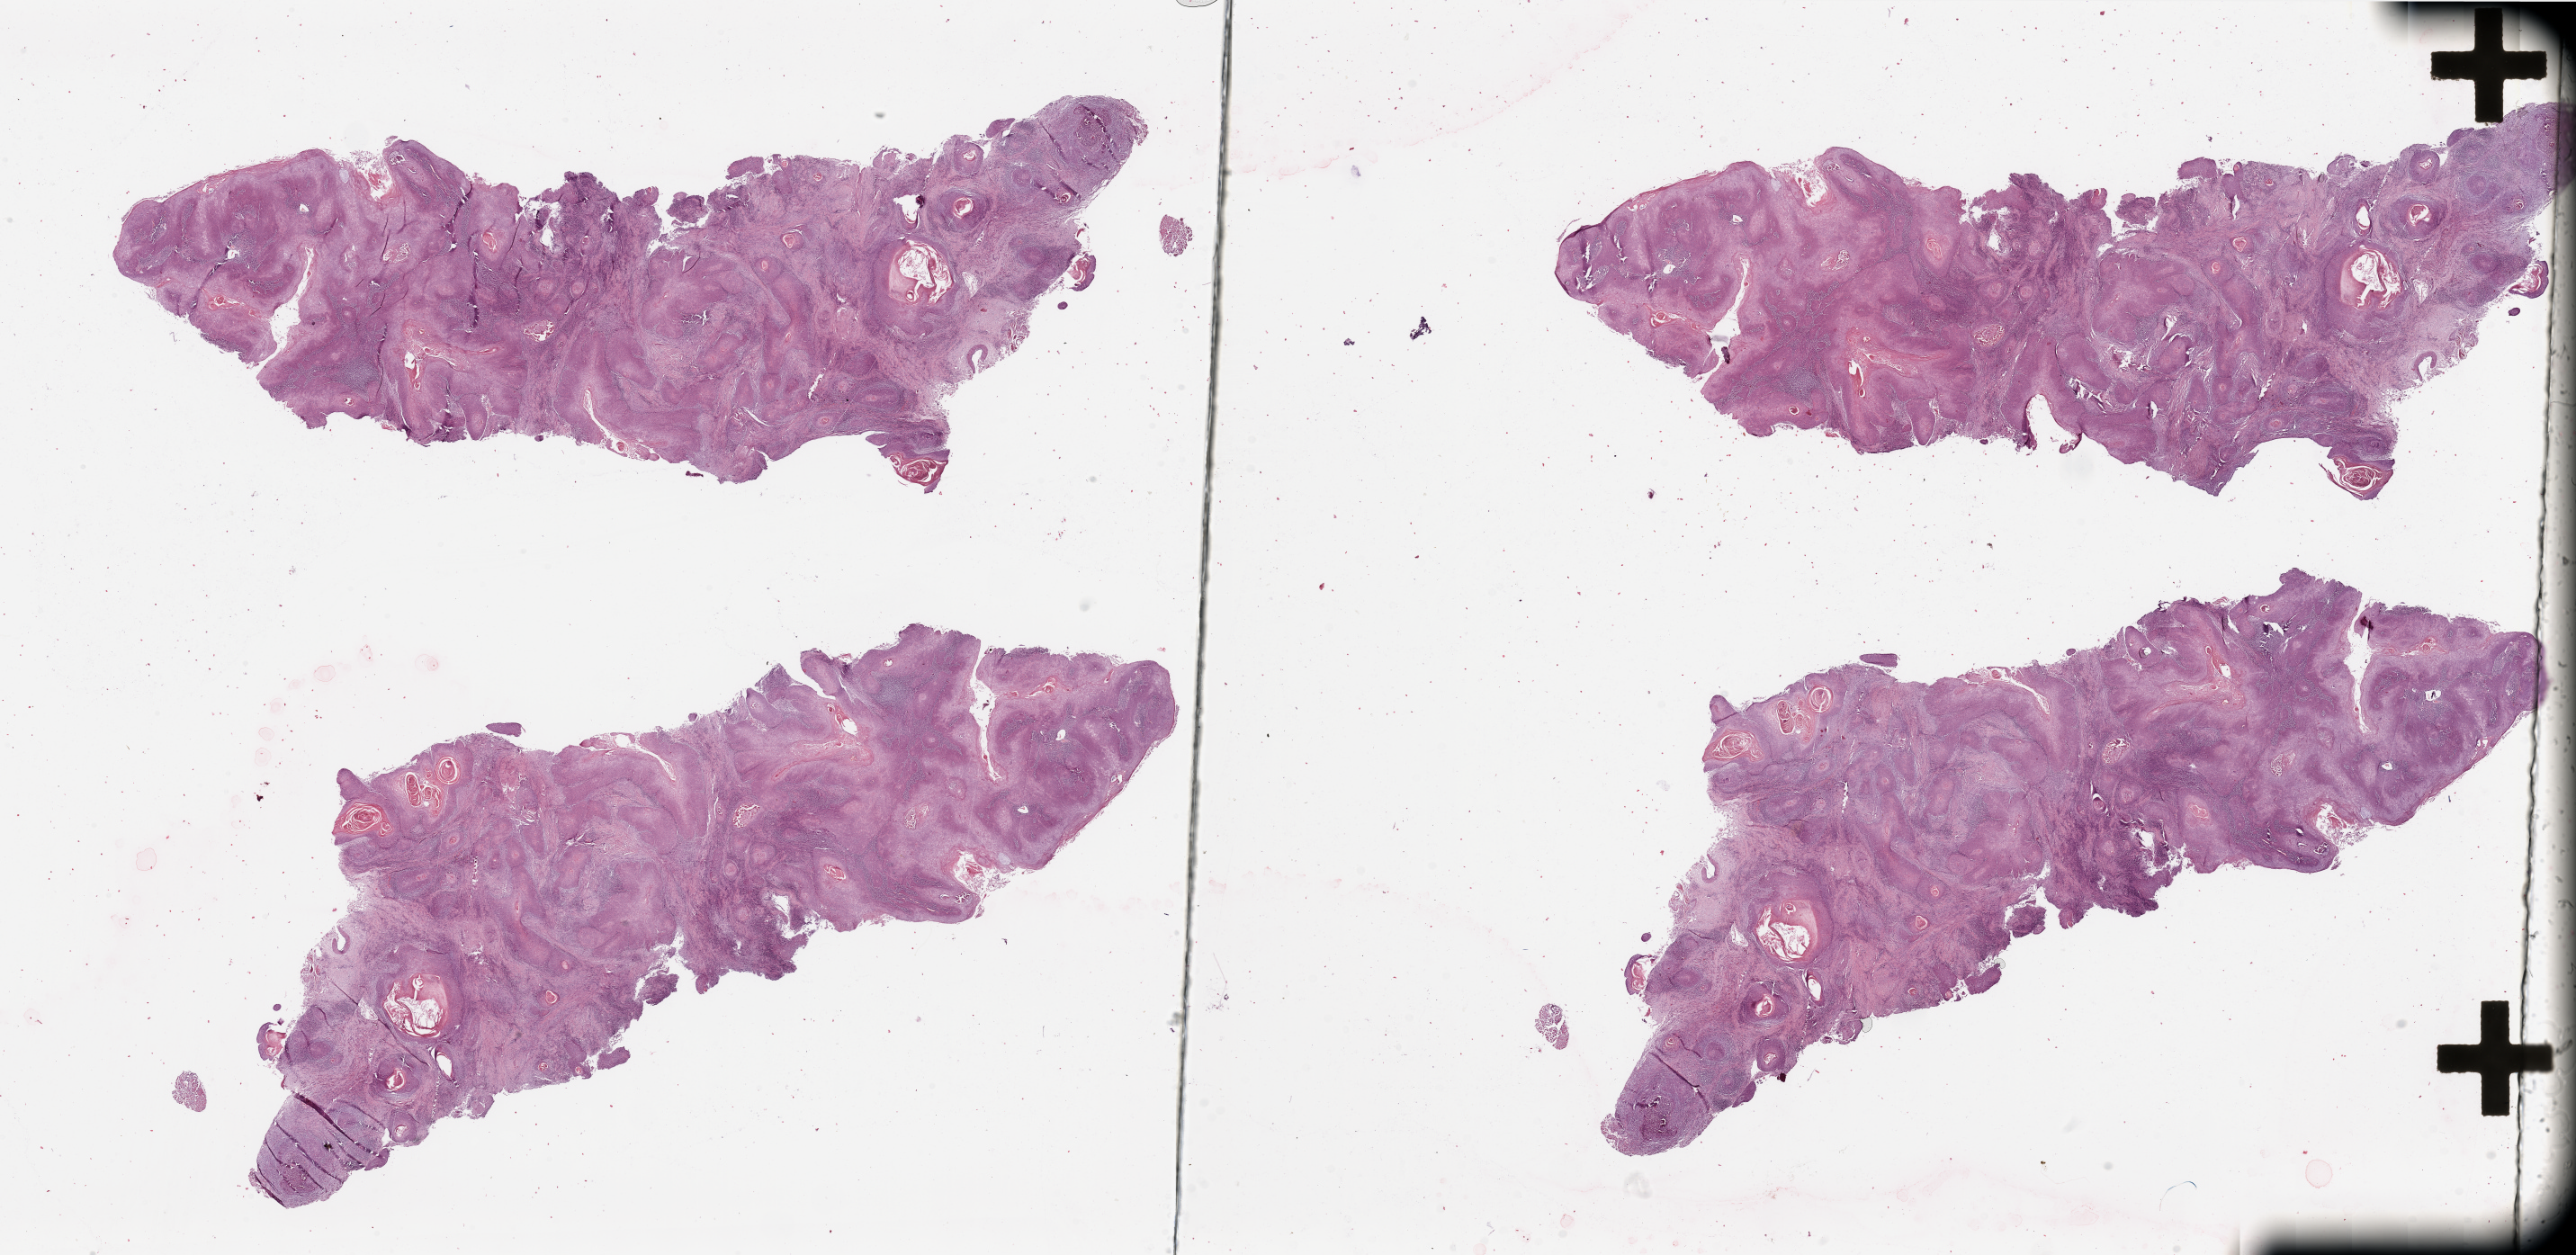
Digitized H&E tissue section (whole slide), a low-resolution overview of the entire scanned area, about 45.3 x 22.1 mm (slide scanned at 20x); tumour tissue sample, sampled site: larynx. Male, 61 y/o. Histologic grade: G2 (moderately differentiated). Pathologist review of this section (percent, as recorded): tumour nuclei 80%, necrosis 3%.
Primary tumour site (as recorded): larynx. AJCC pathologic stage: IVA. Diagnosis: Squamous cell carcinoma, NOS (larynx, NOS).